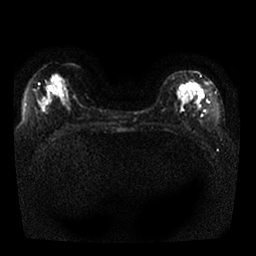
Breast MRI, one axial slice; slice 12 of 25 in the series (ordered by position); diffusion-weighted series; image 2 of 4 stored at this slice position (different b-values; order by instance number); 1.5 T; 4 mm slice thickness; 256 × 256 image matrix, field of view 330 × 330 mm. Female patient.
Outlined on this slice (expert manual segmentation):
- tumour on diffusion-weighted imaging: bounding box [x1, y1, x2, y2] px = [181, 81, 198, 95]